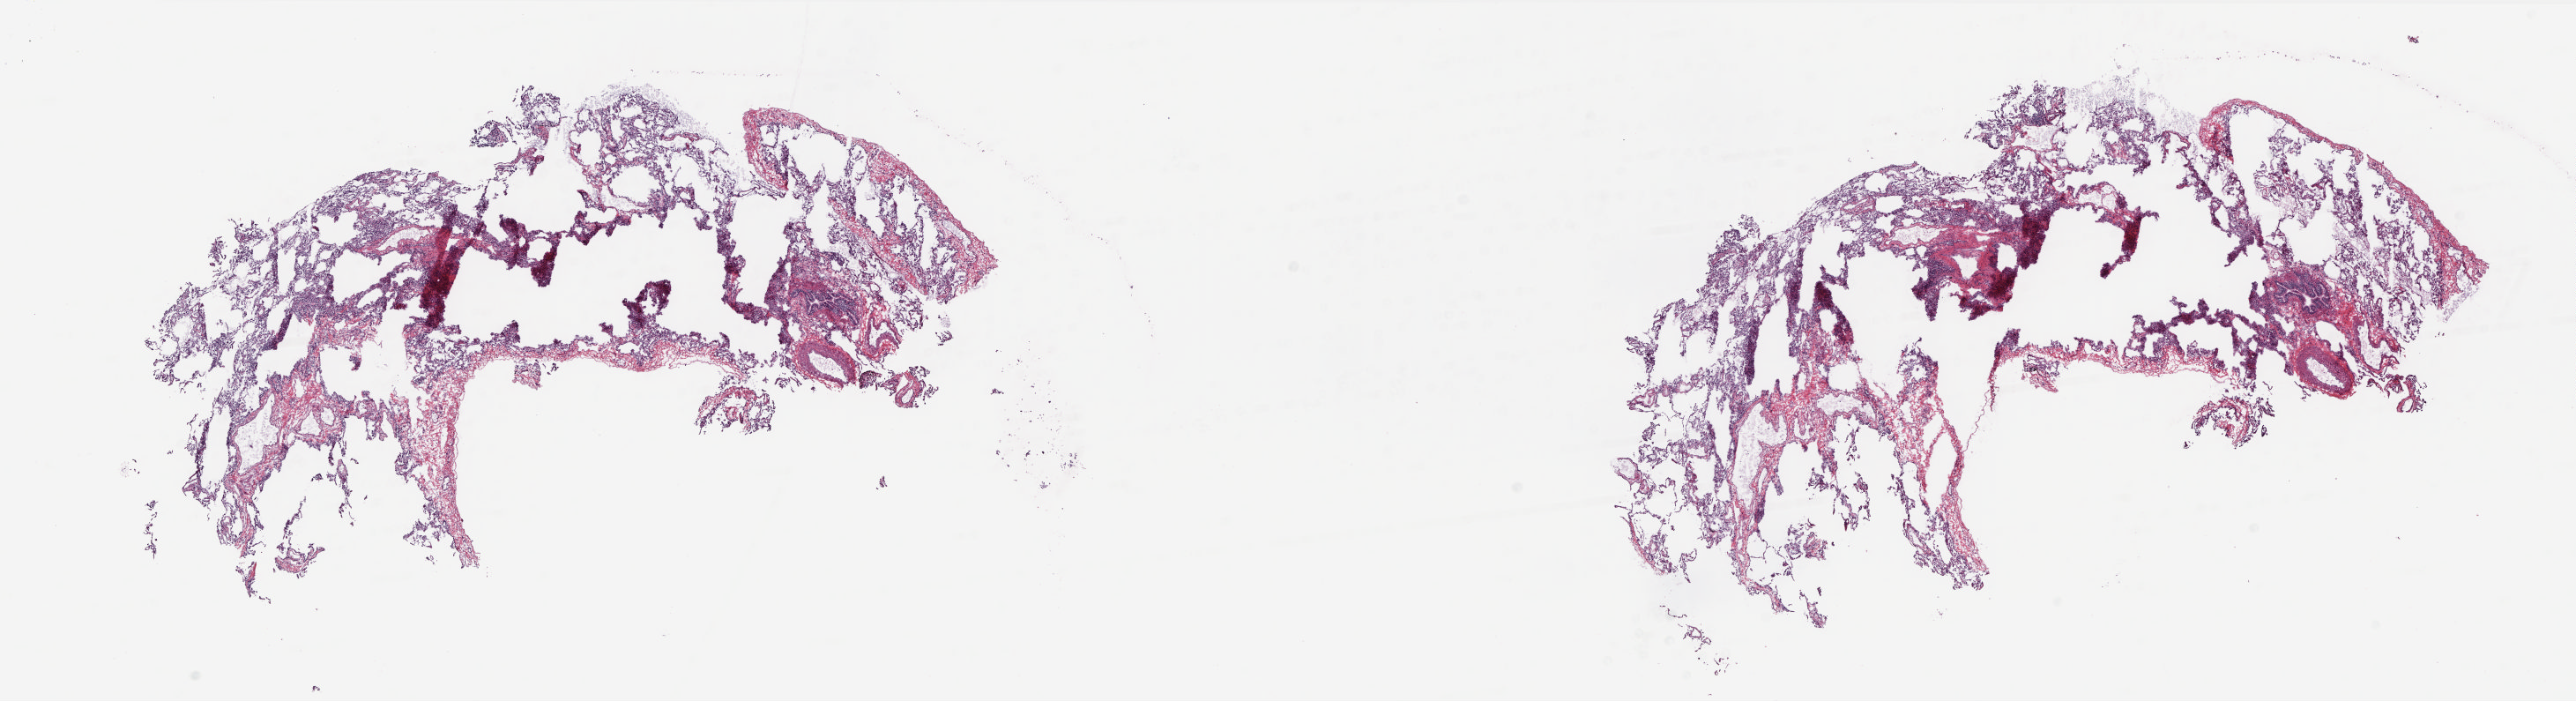
Digitized Hematoxylin and eosin (H&E) stained tissue section (whole slide), a low-resolution overview of the entire scanned area, about 23.6 x 6.4 mm (slide scanned at 20x). Frozen section from the top of the tissue portion. Lung, solid tissue normal (non-tumour tissue) sample. Male, age 64 years at initial diagnosis. Composition of this section per pathologist review: tumour cells 0%, tumour nuclei 0%, normal cells 100%, stromal cells 0%, necrosis 0%. Inflammatory infiltration, as recorded: lymphocyte infiltration 2%, monocyte infiltration 5%, neutrophil infiltration 0%.
- this section: solid tissue normal (non-tumour) sample from the same patient
- patient diagnosis: Mucinous adenocarcinoma (lower lobe, lung)